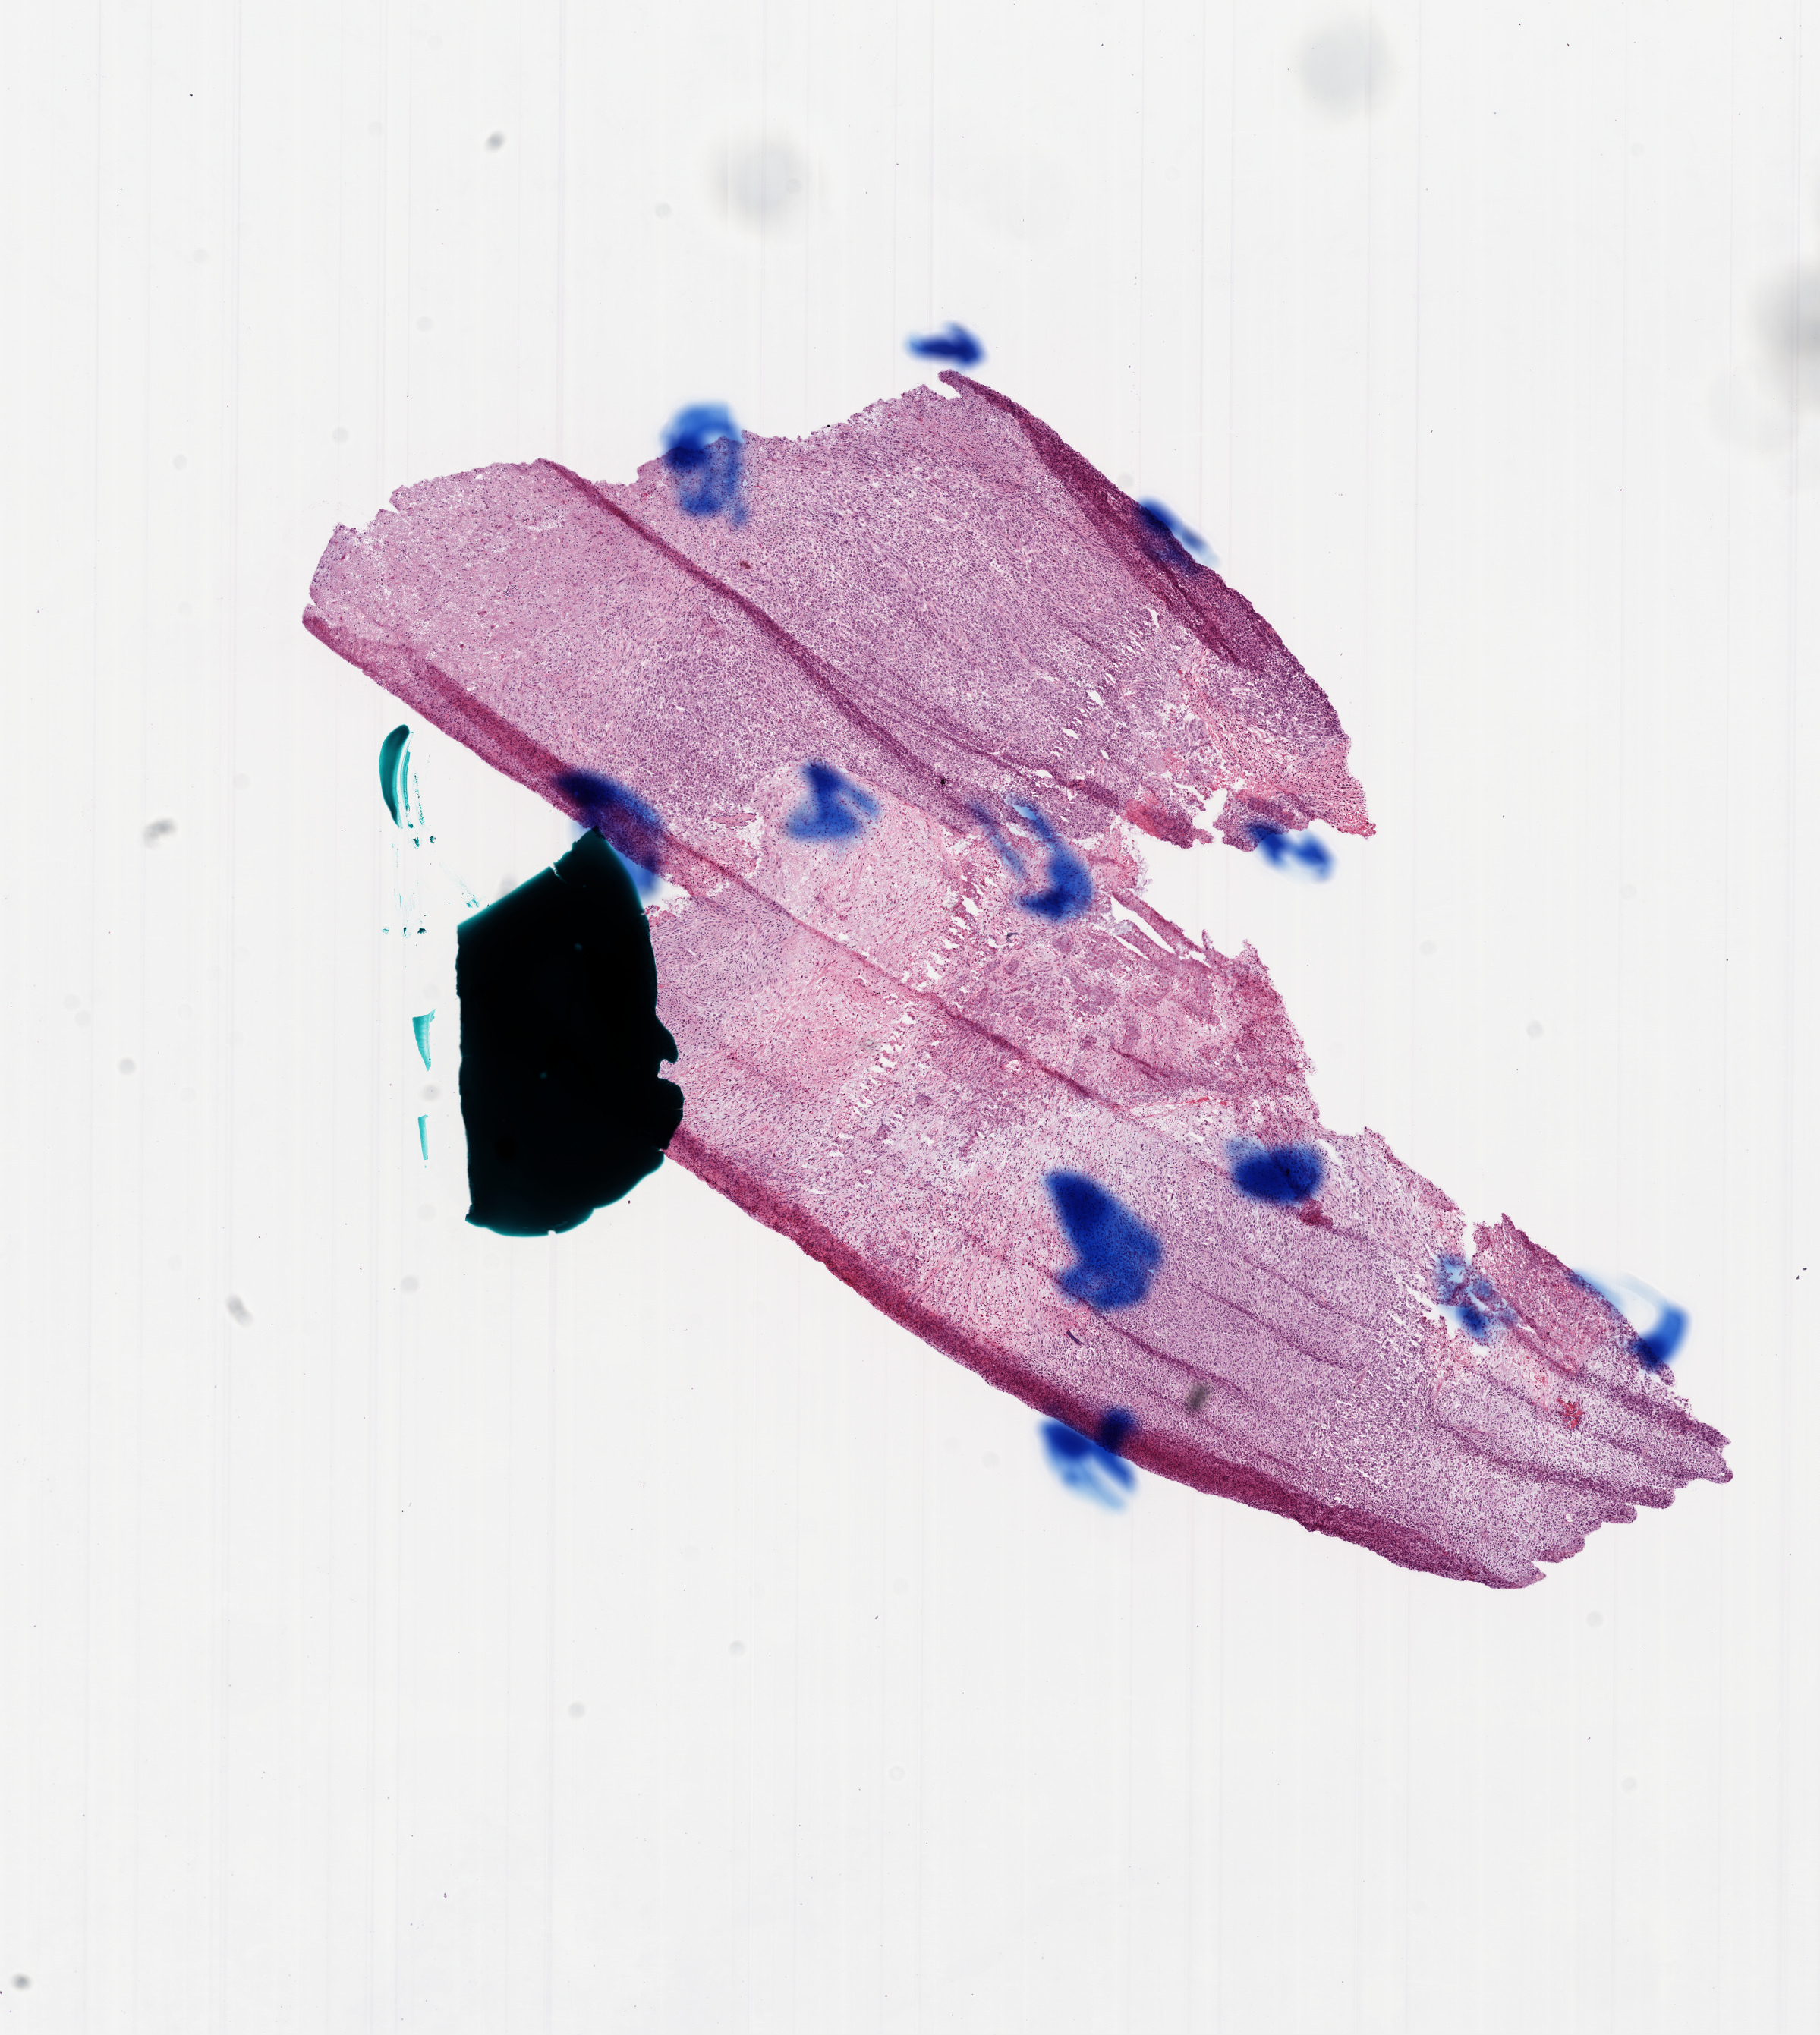
Whole-slide histology image, Hematoxylin and eosin (H&E) stained — whole scanned area (about 9.7 x 10.8 mm, slide scanned at 20x) shown as a low-resolution overview, frozen section, primary tumour sample from the brain. Male patient; age at initial diagnosis 71 years. Slide review estimates, as recorded: tumour cells 70%, tumour nuclei 95%, normal cells 0%, stromal cells 10%, necrosis 20%.
Histologic diagnosis: Glioblastoma.